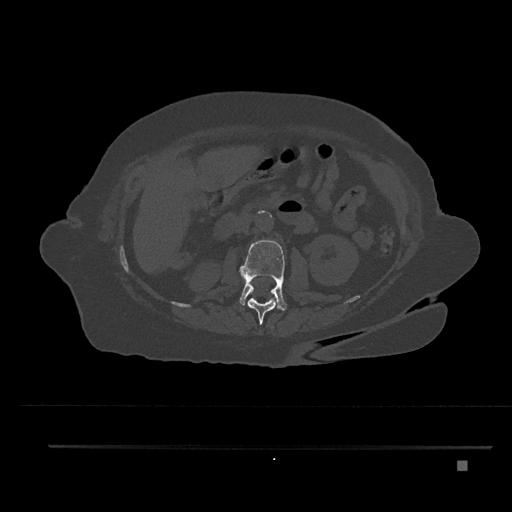
CT including the spine, one axial slice; position 196 of 797 along the scan axis; bone window (W 1800 / L 400 HU); 0.5 mm slice thickness; 512 × 512 image matrix, field of view 437 × 437 mm. Female patient, age 76 years. Case-level facts recorded for this patient, not image findings: primary cancer: lung; vertebrae with lytic lesions (as recorded): T11, L3.
Annotated regions visible in this slice (semi-automatically segmented with operator editing):
- L1 vertebra: bounding box [x1, y1, x2, y2] px = [248, 298, 278, 325]
- L2 vertebra: [239, 239, 287, 311]